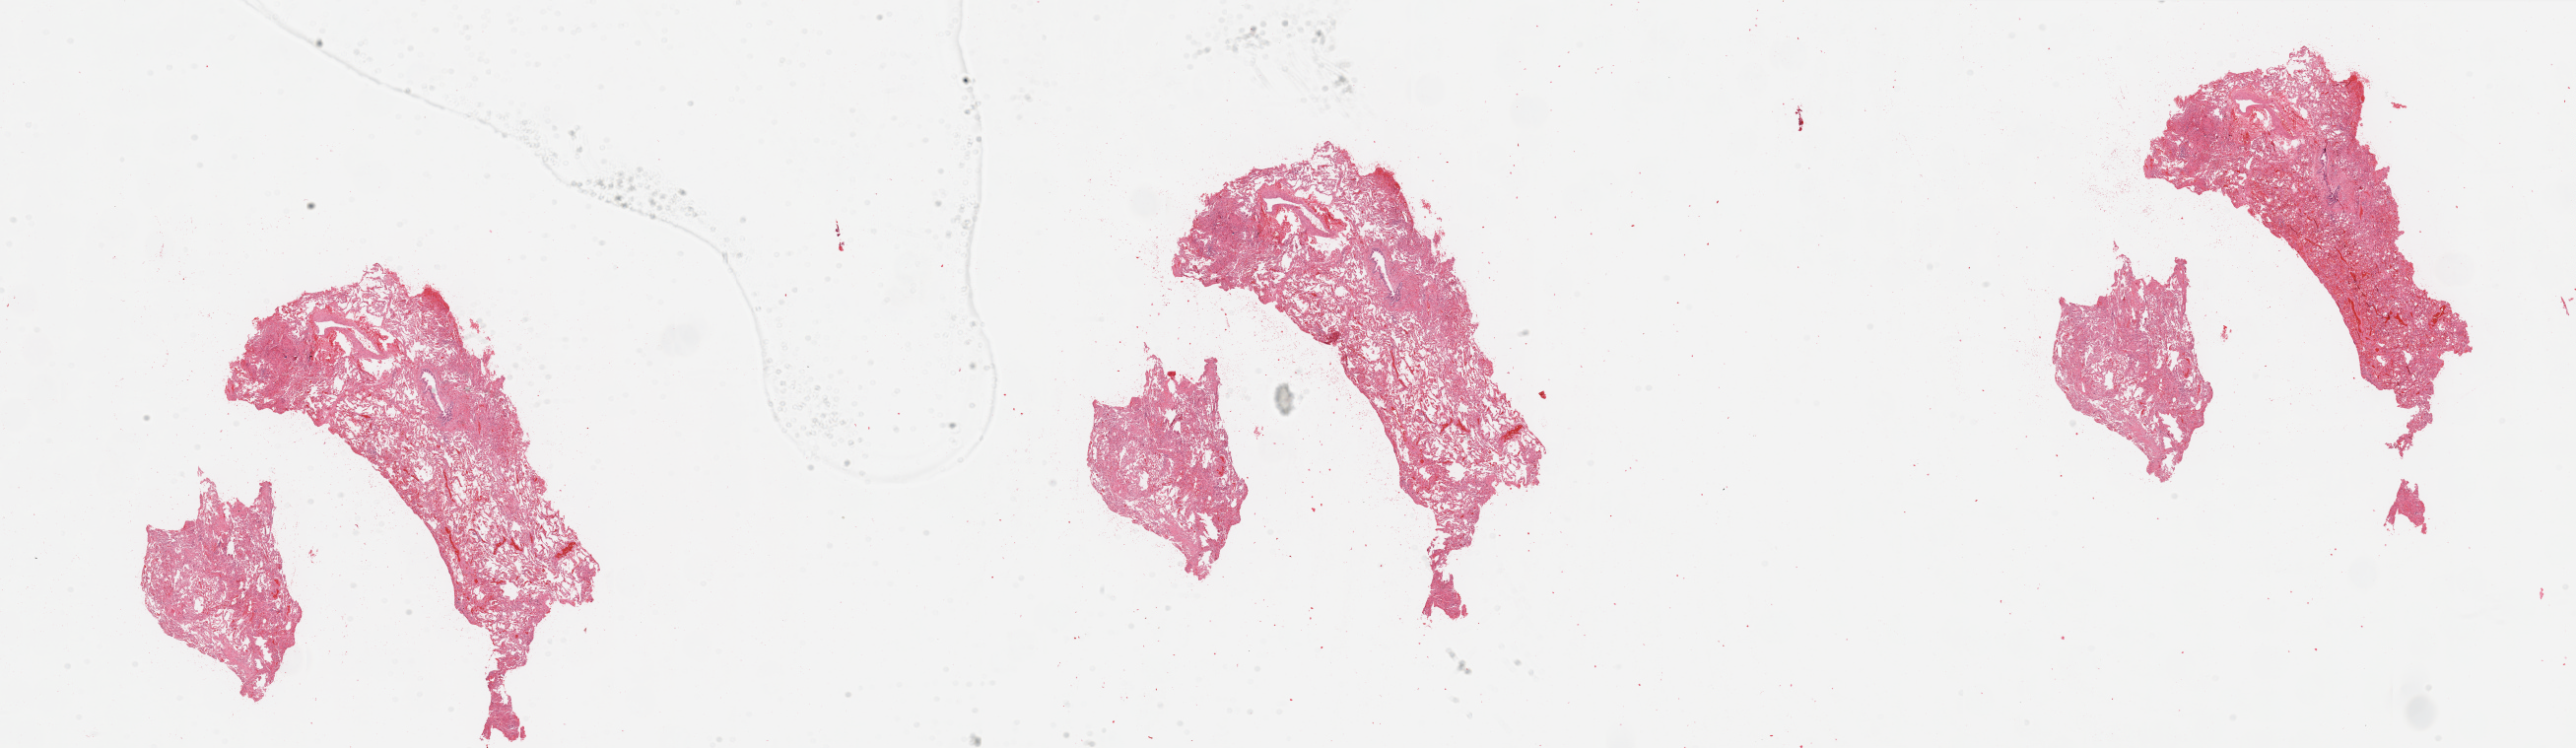
H&E whole-slide image, low-resolution overview of the scanned area, about 41.3 x 12.0 mm, normal (non-tumour) tissue sample, sampled site: lung. Male, 65 y/o.
* this section: normal (non-tumour) tissue from the same patient
* patient diagnosis: Adenocarcinoma, NOS